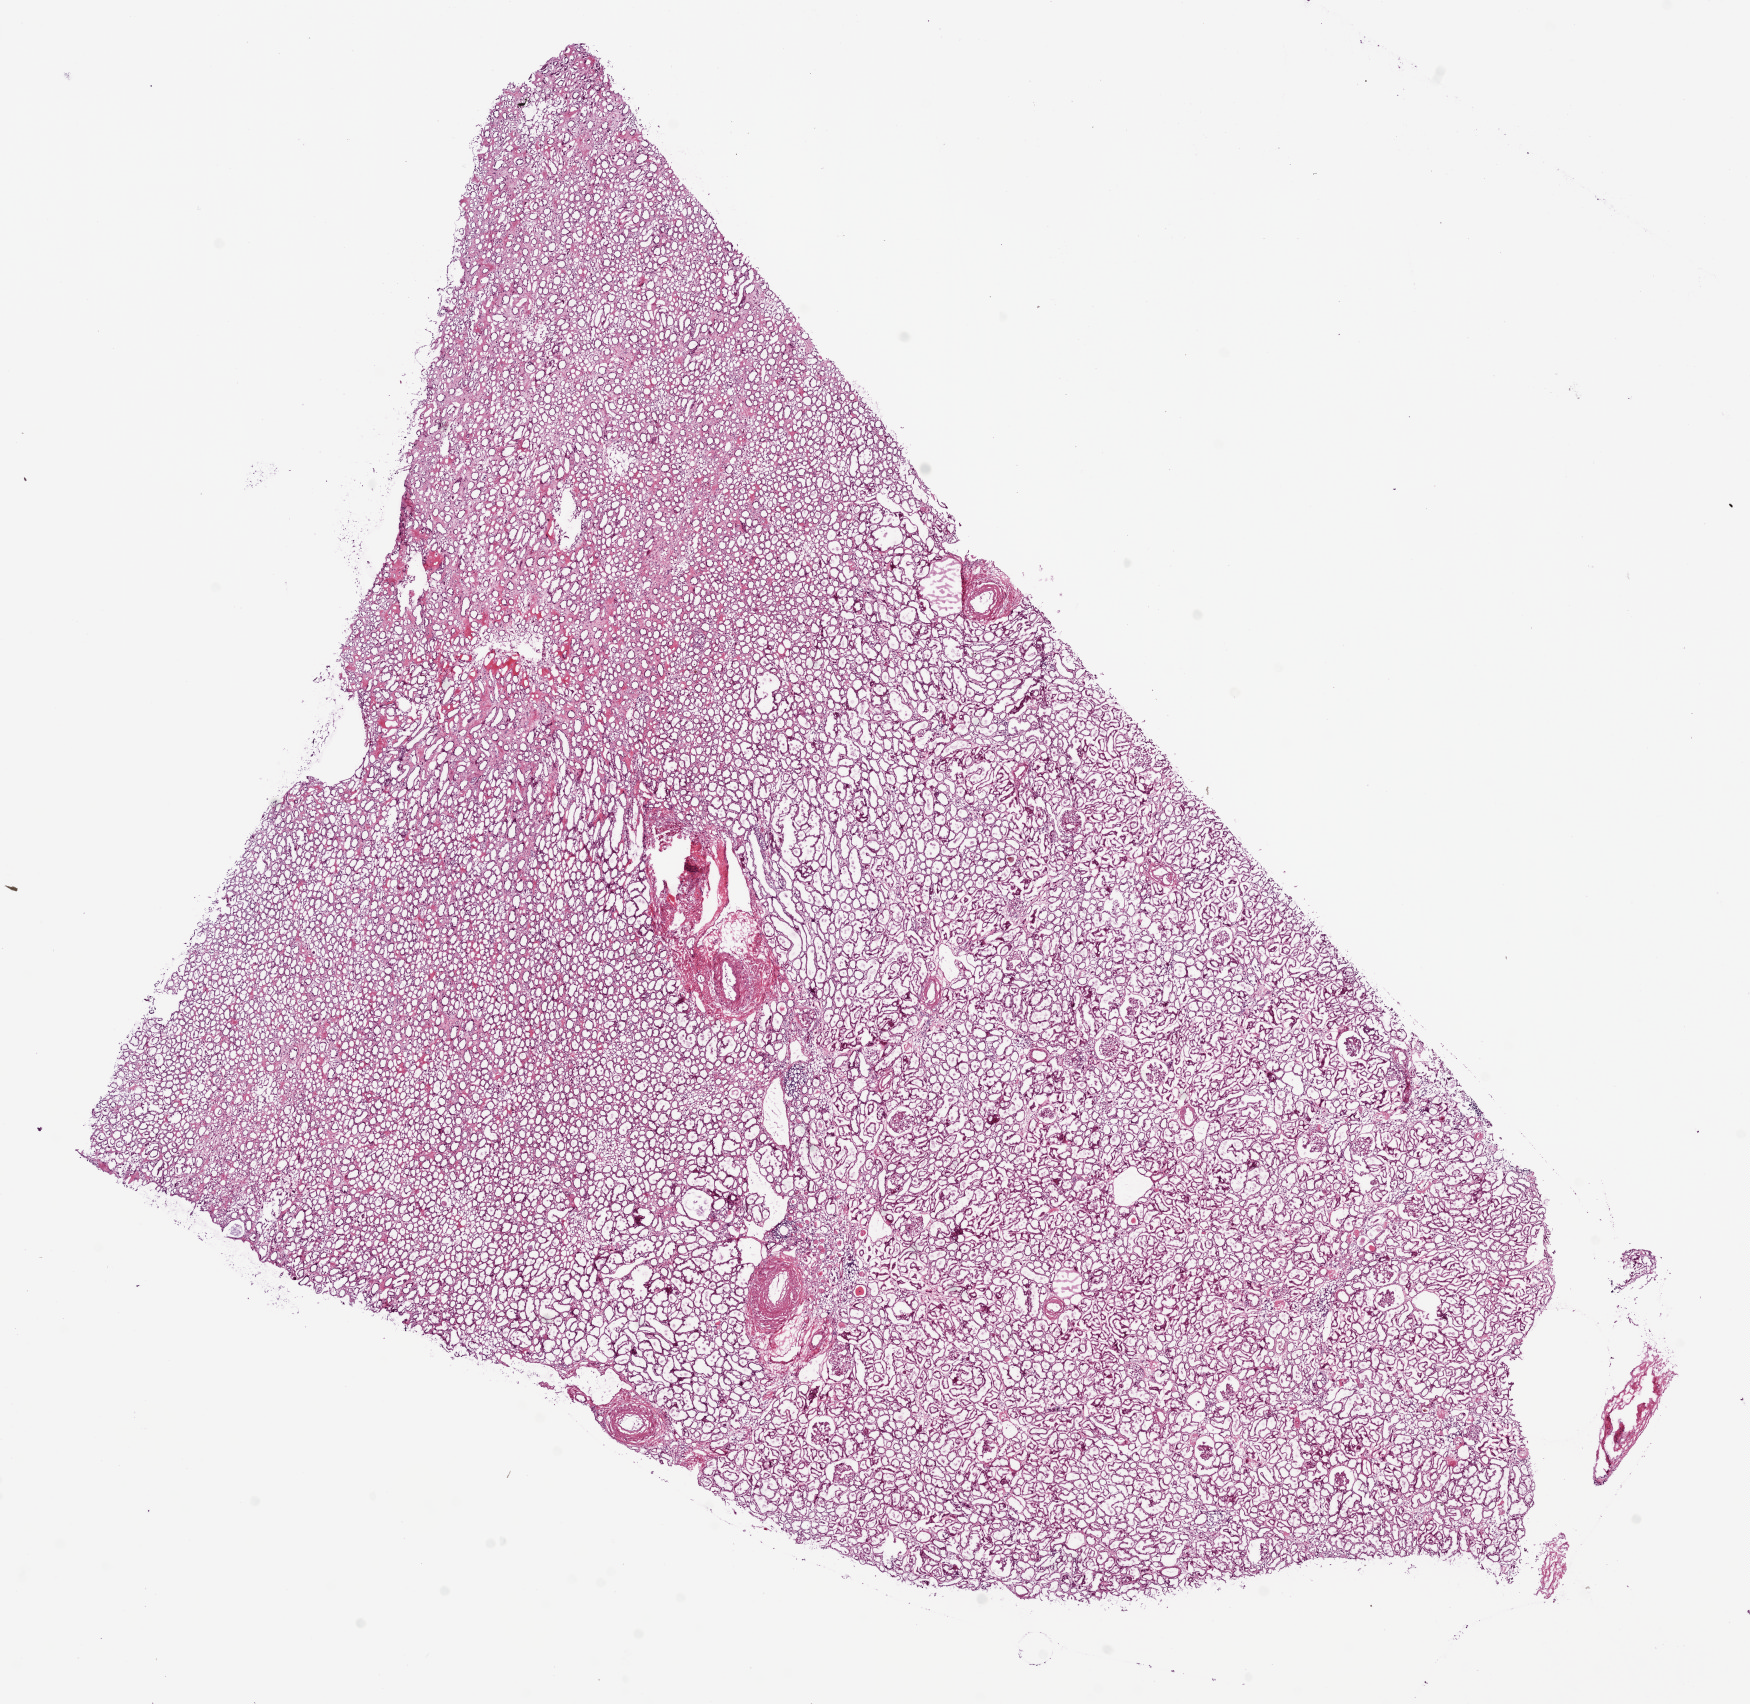
Digitized H&E tissue section (whole slide), low-resolution overview of the scanned area, about 14.0 x 13.7 mm. Frozen section from the bottom of the tissue portion. Solid tissue normal (non-tumour tissue) sample from the kidney. Male patient; age at initial diagnosis 81 years.
This section: solid tissue normal (non-tumour) sample from the same patient. Patient diagnosis: Clear cell adenocarcinoma, NOS.